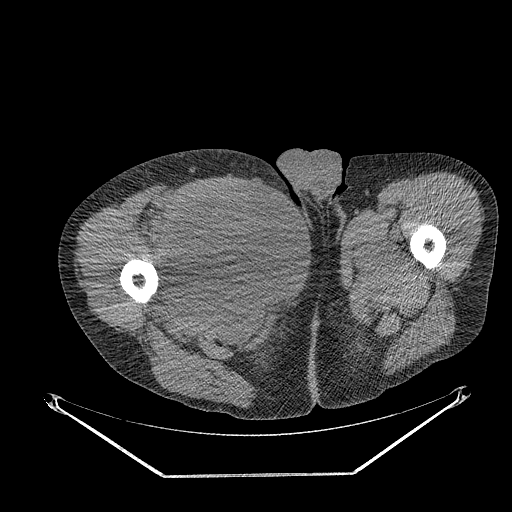
CT of an extremity soft-tissue mass (from a PET/CT study), one axial slice; slice 277 of 311 in the series (ordered by position); soft-tissue window (W 400 / L 40 HU); 3.75 mm slice thickness; 512 × 512 image matrix, field of view 500 × 500 mm. Male patient. From the clinical record (not read from this slice): histological type: undifferentiated - pleiomorphic; grade: high; site of the primary tumour: right thigh.
Structures marked on this image (expert contour drawn on MRI and transferred to this co-registered scan by the dataset authors):
- gross tumour volume including surrounding oedema: bounding box <167,181,264,279> (left, top, right, bottom; pixels)
- gross tumour volume (mass): <167,183,264,279>